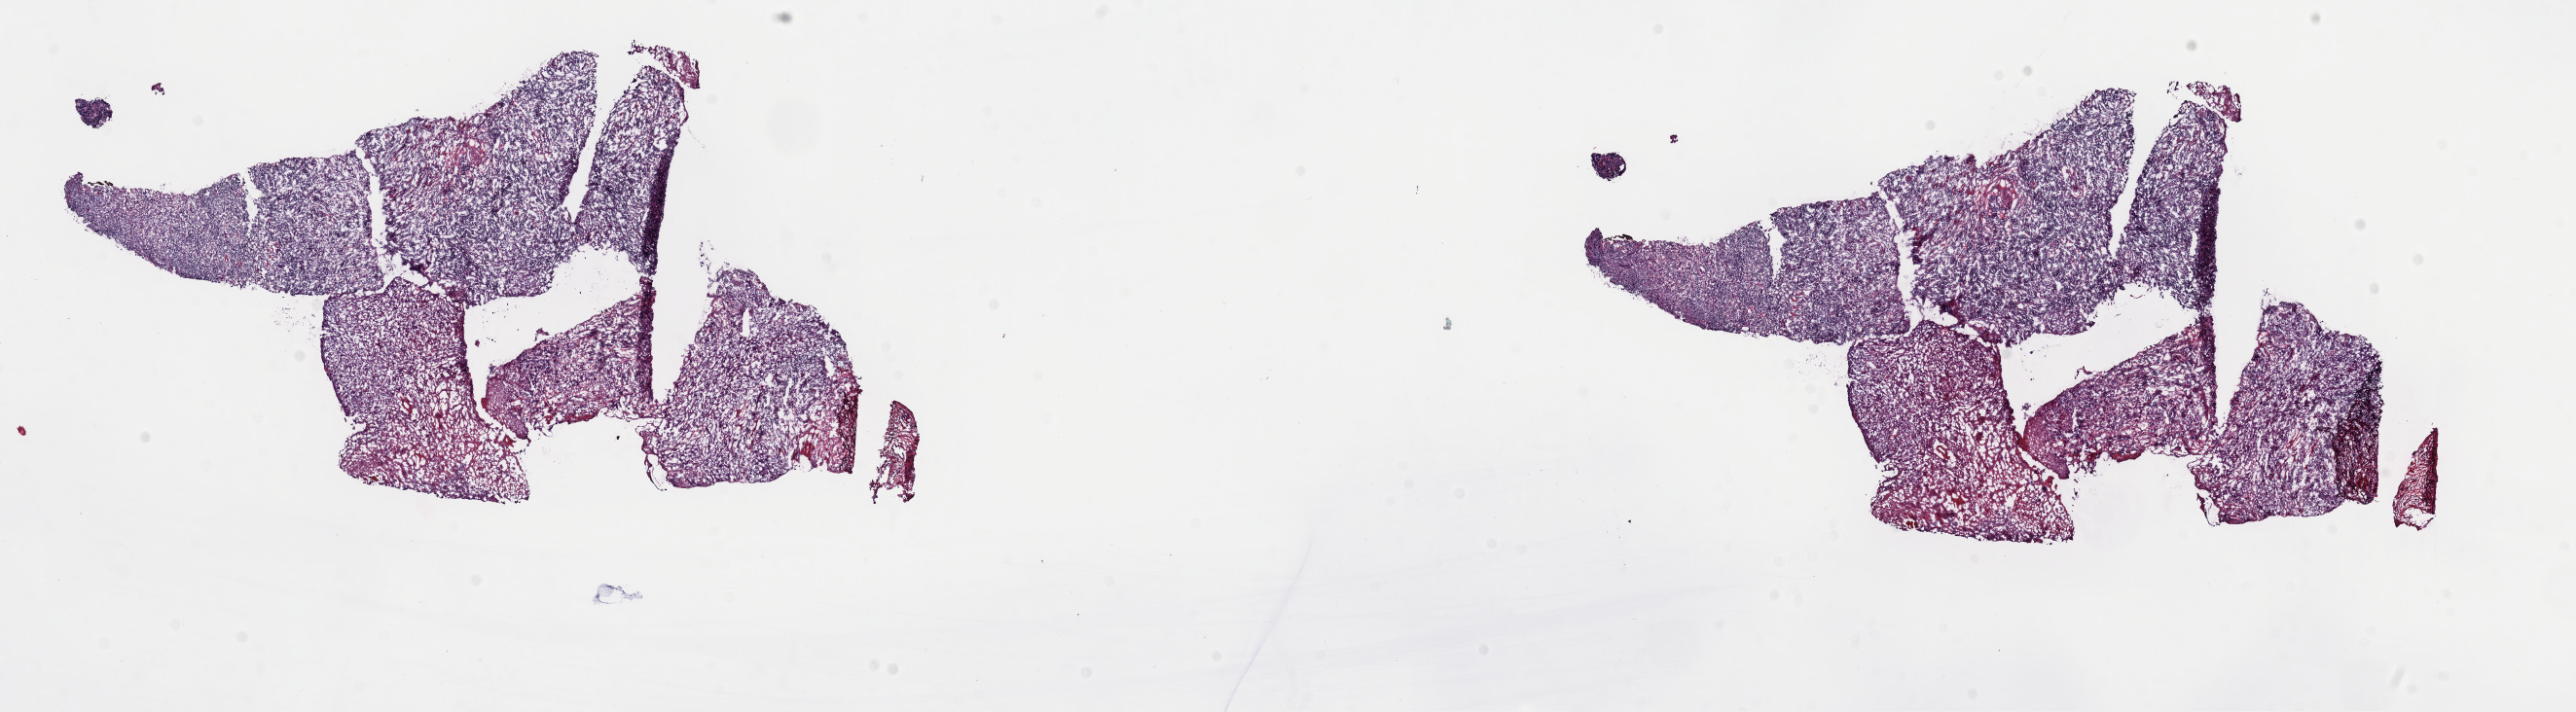
H&E-stained whole-slide image, whole scanned area (about 20.9 x 5.8 mm, from a 40x scan) shown as a low-resolution overview, frozen section from the top of the tissue portion, sample: primary tumour, head and neck. Female, age 64 years at initial diagnosis. Histologic grade: G3 (poorly differentiated). Composition of this section per pathologist review: tumour cells 100%, tumour nuclei 100%, normal cells 0%, stromal cells 0%, necrosis 0%. Infiltration values recorded for this section: lymphocyte infiltration 0%, monocyte infiltration 0%, neutrophil infiltration 0%.
* laterality: right
* pathologic diagnosis: Squamous cell carcinoma, NOS